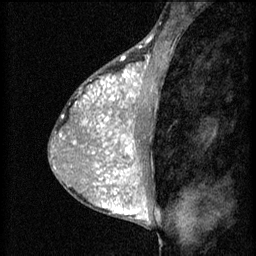
Breast MRI (dynamic contrast-enhanced), one sagittal slice; slice 31 of 60 in the series (ordered by position); 3 images stored at this slice position (order not interpretable as contrast timing); 1.5 T; TE 4.2 ms, TR 8.2 ms; 2 mm slice thickness; 256 × 256 image matrix, field of view 180 × 180 mm. Patient: female, 38 years.
Outlined on this slice (semi-automatic segmentation, software-assisted and operator-edited):
- analysis volume of interest (the breast-tissue region the enhancement analysis was run in; not a lesion): bounding box <95,106,153,171> (left, top, right, bottom; pixels)
- tumour enhancement mask (voxels above the 70 % enhancement threshold inside the analysis volume of interest): <95,106,141,171>